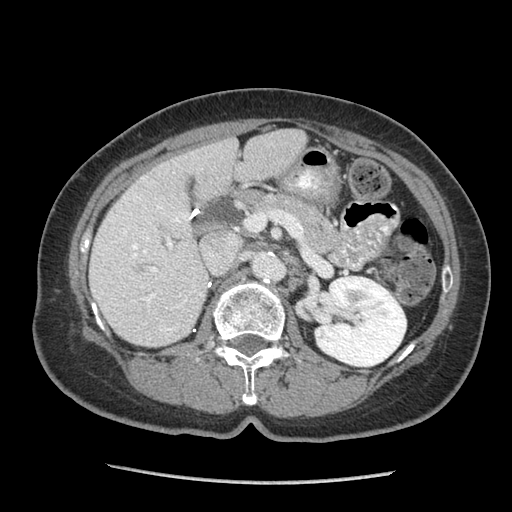
Contrast-enhanced abdominal CT (liver protocol), one axial slice. Position 39 of 105 along the scan axis. Reconstruction kernel STANDARD. Soft-tissue window (W 400 / L 40 HU). 512 × 512 image matrix, field of view 340 × 340 mm. From the clinical record (not read from this slice): diagnosis: hepatocellular carcinoma (patient treated with transarterial chemoembolisation; whether this scan precedes or follows treatment is not stated here); TNM stage (as recorded): Stage-I; Child-Pugh class: A; tumour size: 11.1 cm.
Outlined on this slice (semi-automatic segmentation, software-assisted and operator-edited):
- liver parenchyma outside the tumour (the mass and vessels are separate outlines, so this box may not span the whole liver): bounding box (x1, y1, x2, y2) in pixels: (90, 128, 306, 346)
- liver vessels: (110, 178, 202, 332)